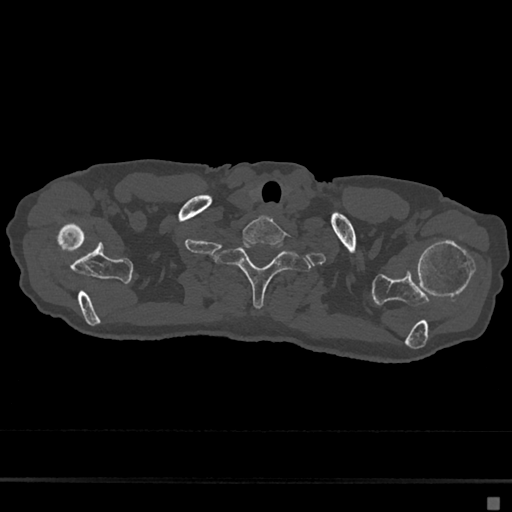
CT including the spine, one axial slice; position 615 of 797 along the scan axis; reconstruction kernel Br40s/3; 120 kVp; bone window (W 1800 / L 400 HU); 512 × 512 image matrix. Patient: female, 68 years. From the clinical record (not read from this slice): primary cancer: renal.
Outlined on this slice (semi-automatically segmented with operator editing):
- T1 vertebra: bounding box [x1, y1, x2, y2] px = [215, 239, 312, 307]